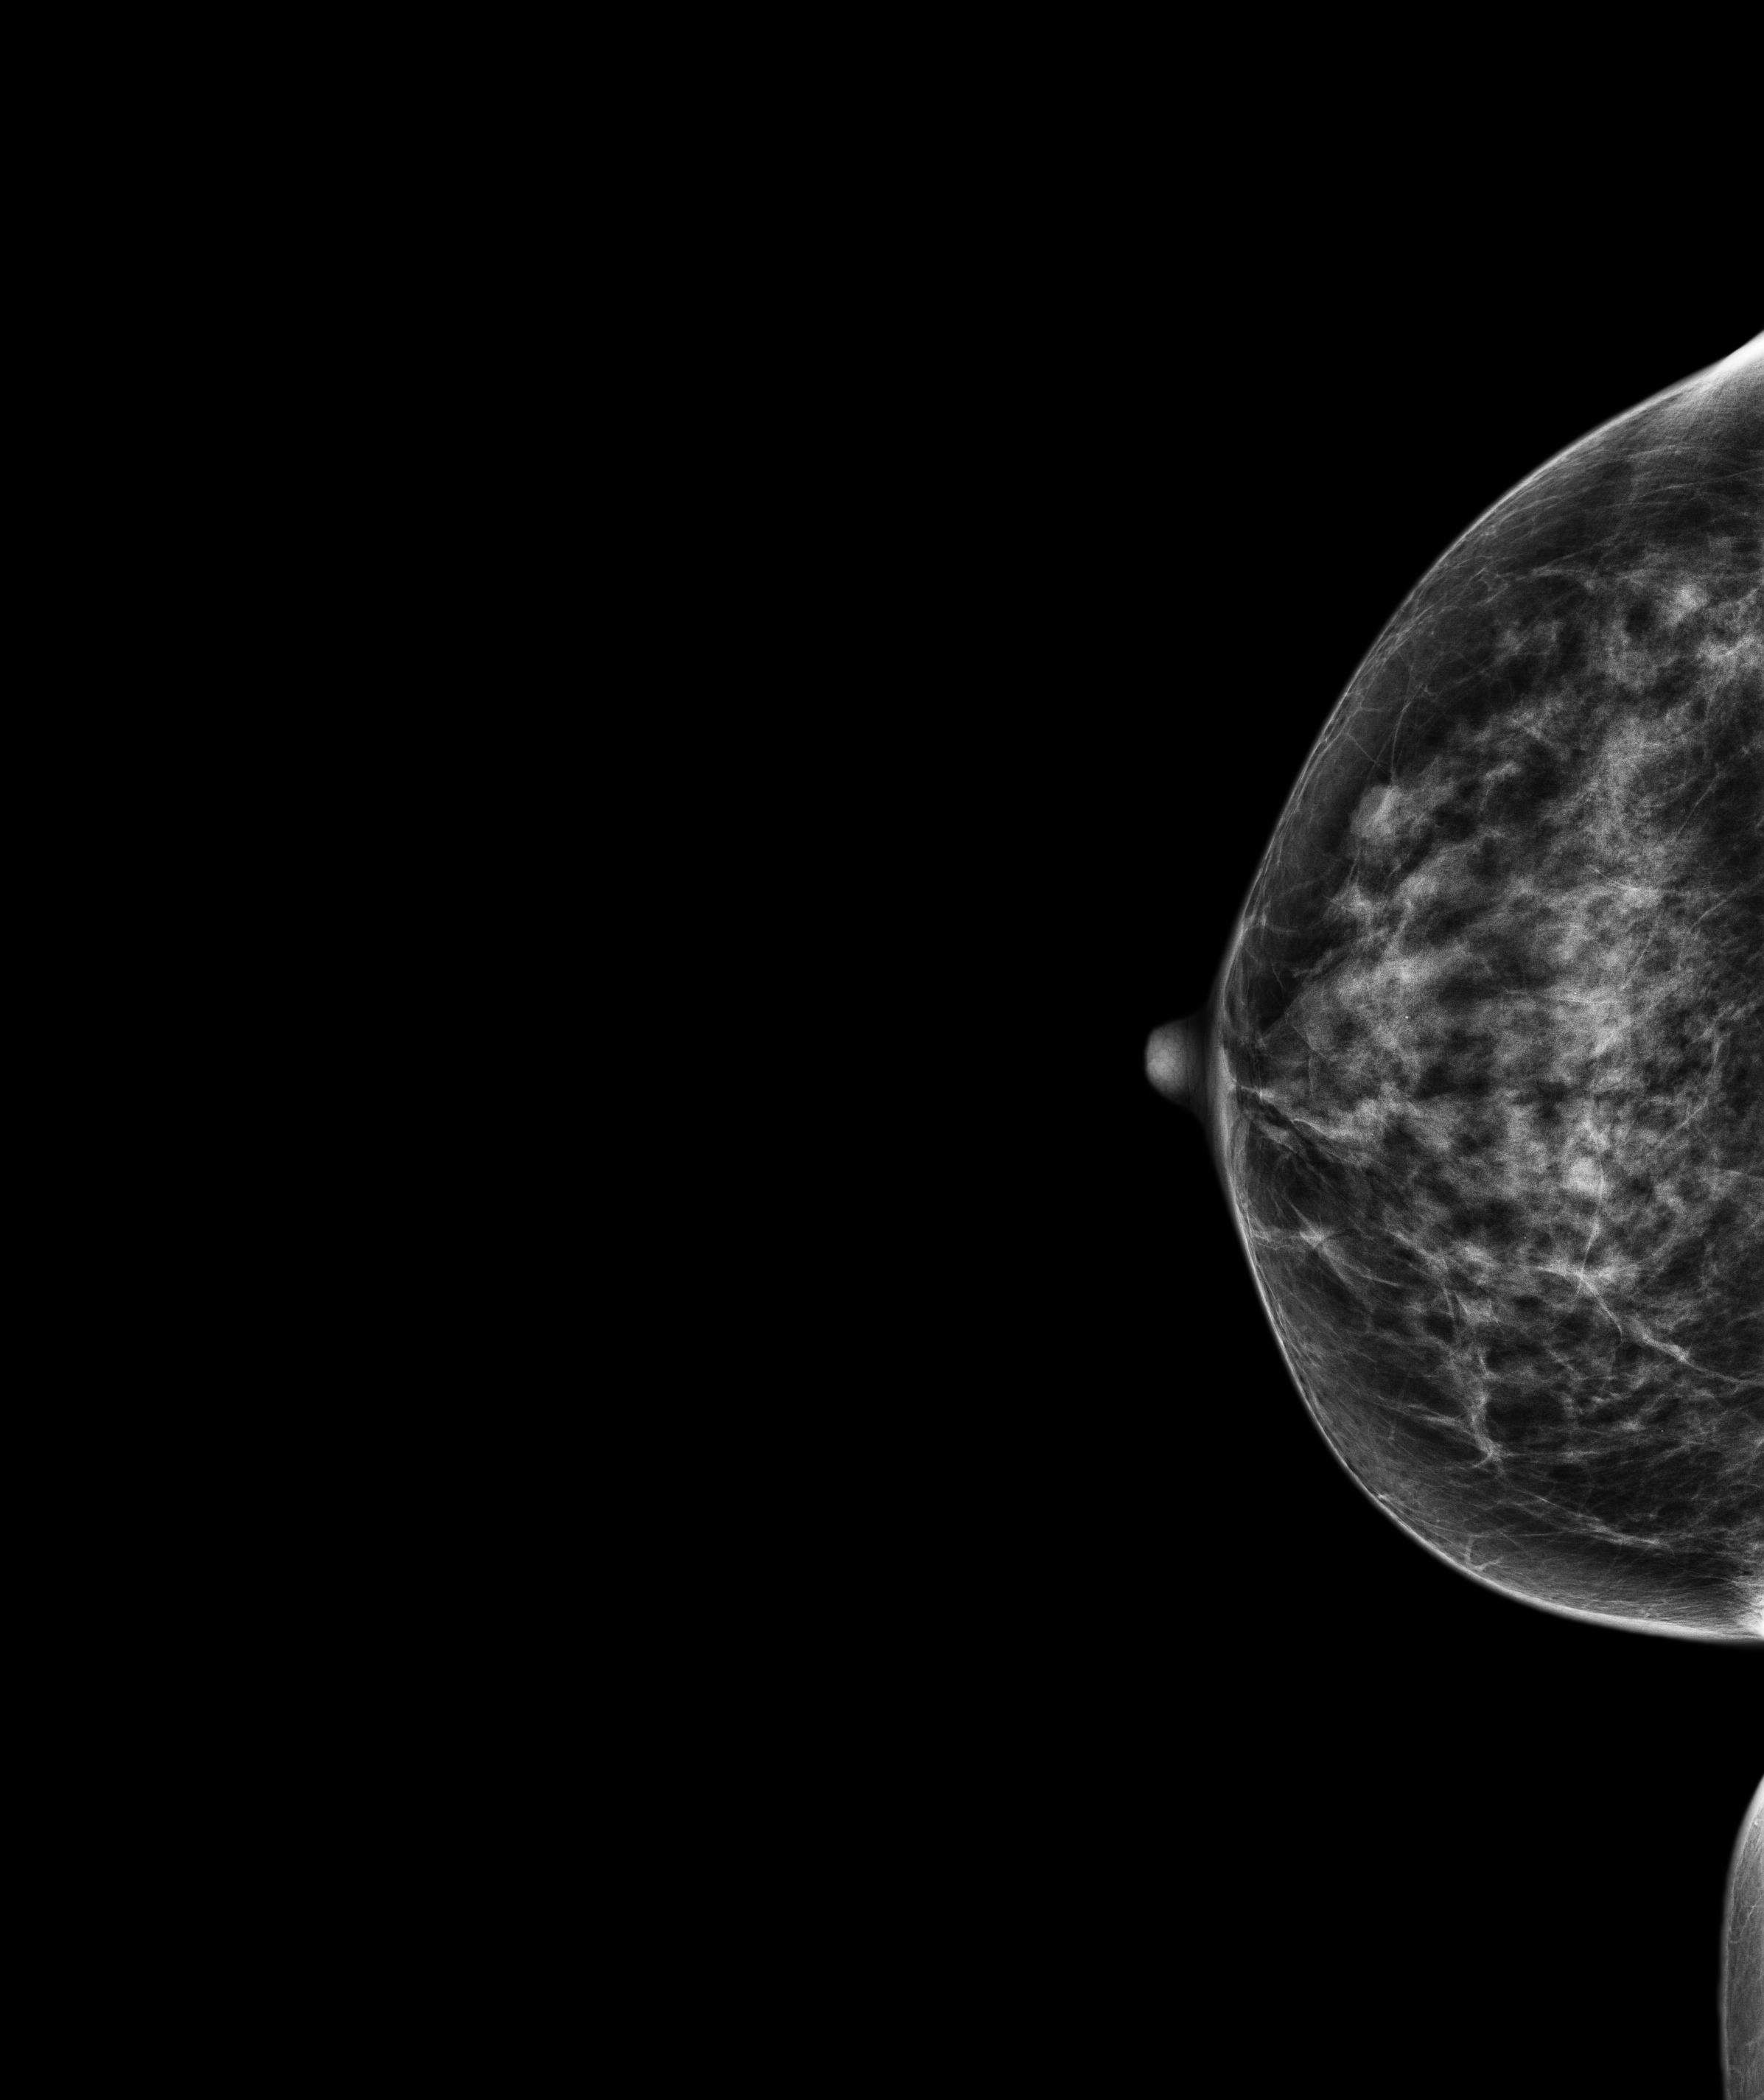
Annual screening mammography examination, system: Senographe Pristina. Female patient, age 59 years.
Image type: full-field digital mammogram. Breast: right. Projection: CC view.